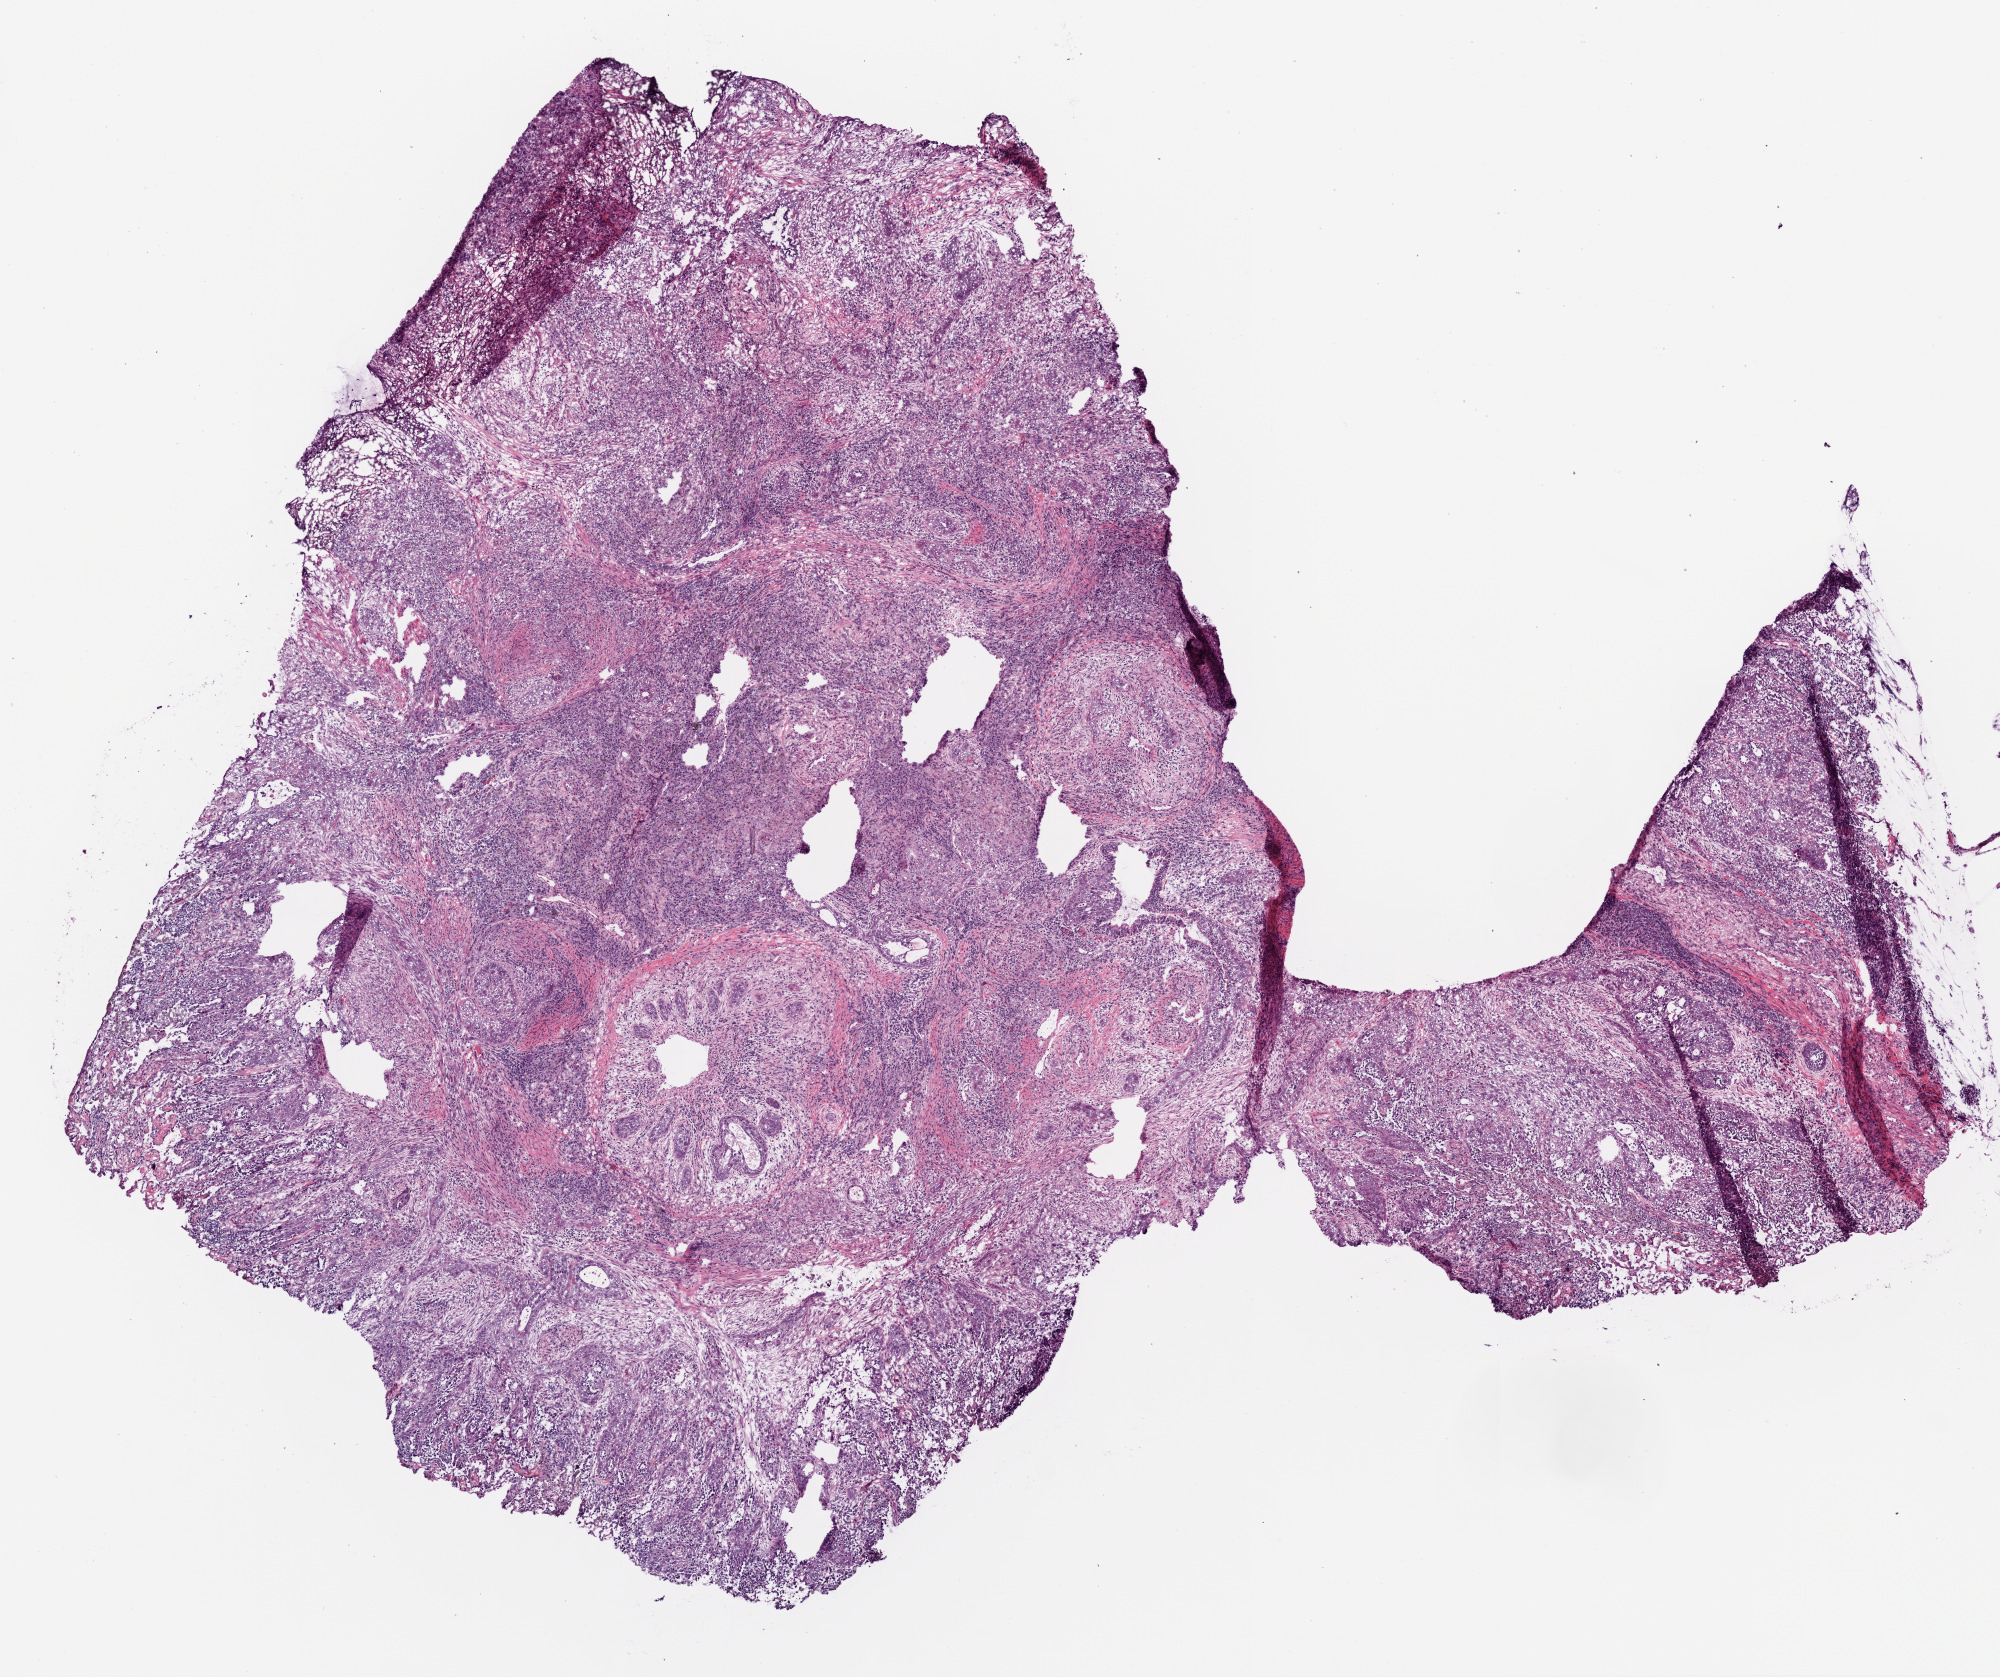
Hematoxylin and eosin (H&E) stained whole-slide image, low-resolution overview of the scanned area, about 8.0 x 6.7 mm (slide scanned at 20x); frozen section from the top of the tissue portion; sample: primary tumour, lung. Female, age 62 years at initial diagnosis. Composition of this section per pathologist review: tumour cells 87%, tumour nuclei 70%, normal cells 0%, stromal cells 10%, necrosis 3%.
Pathologic diagnosis: Squamous cell carcinoma, NOS (lower lobe, lung). Laterality: right. AJCC pathologic stage: IA.